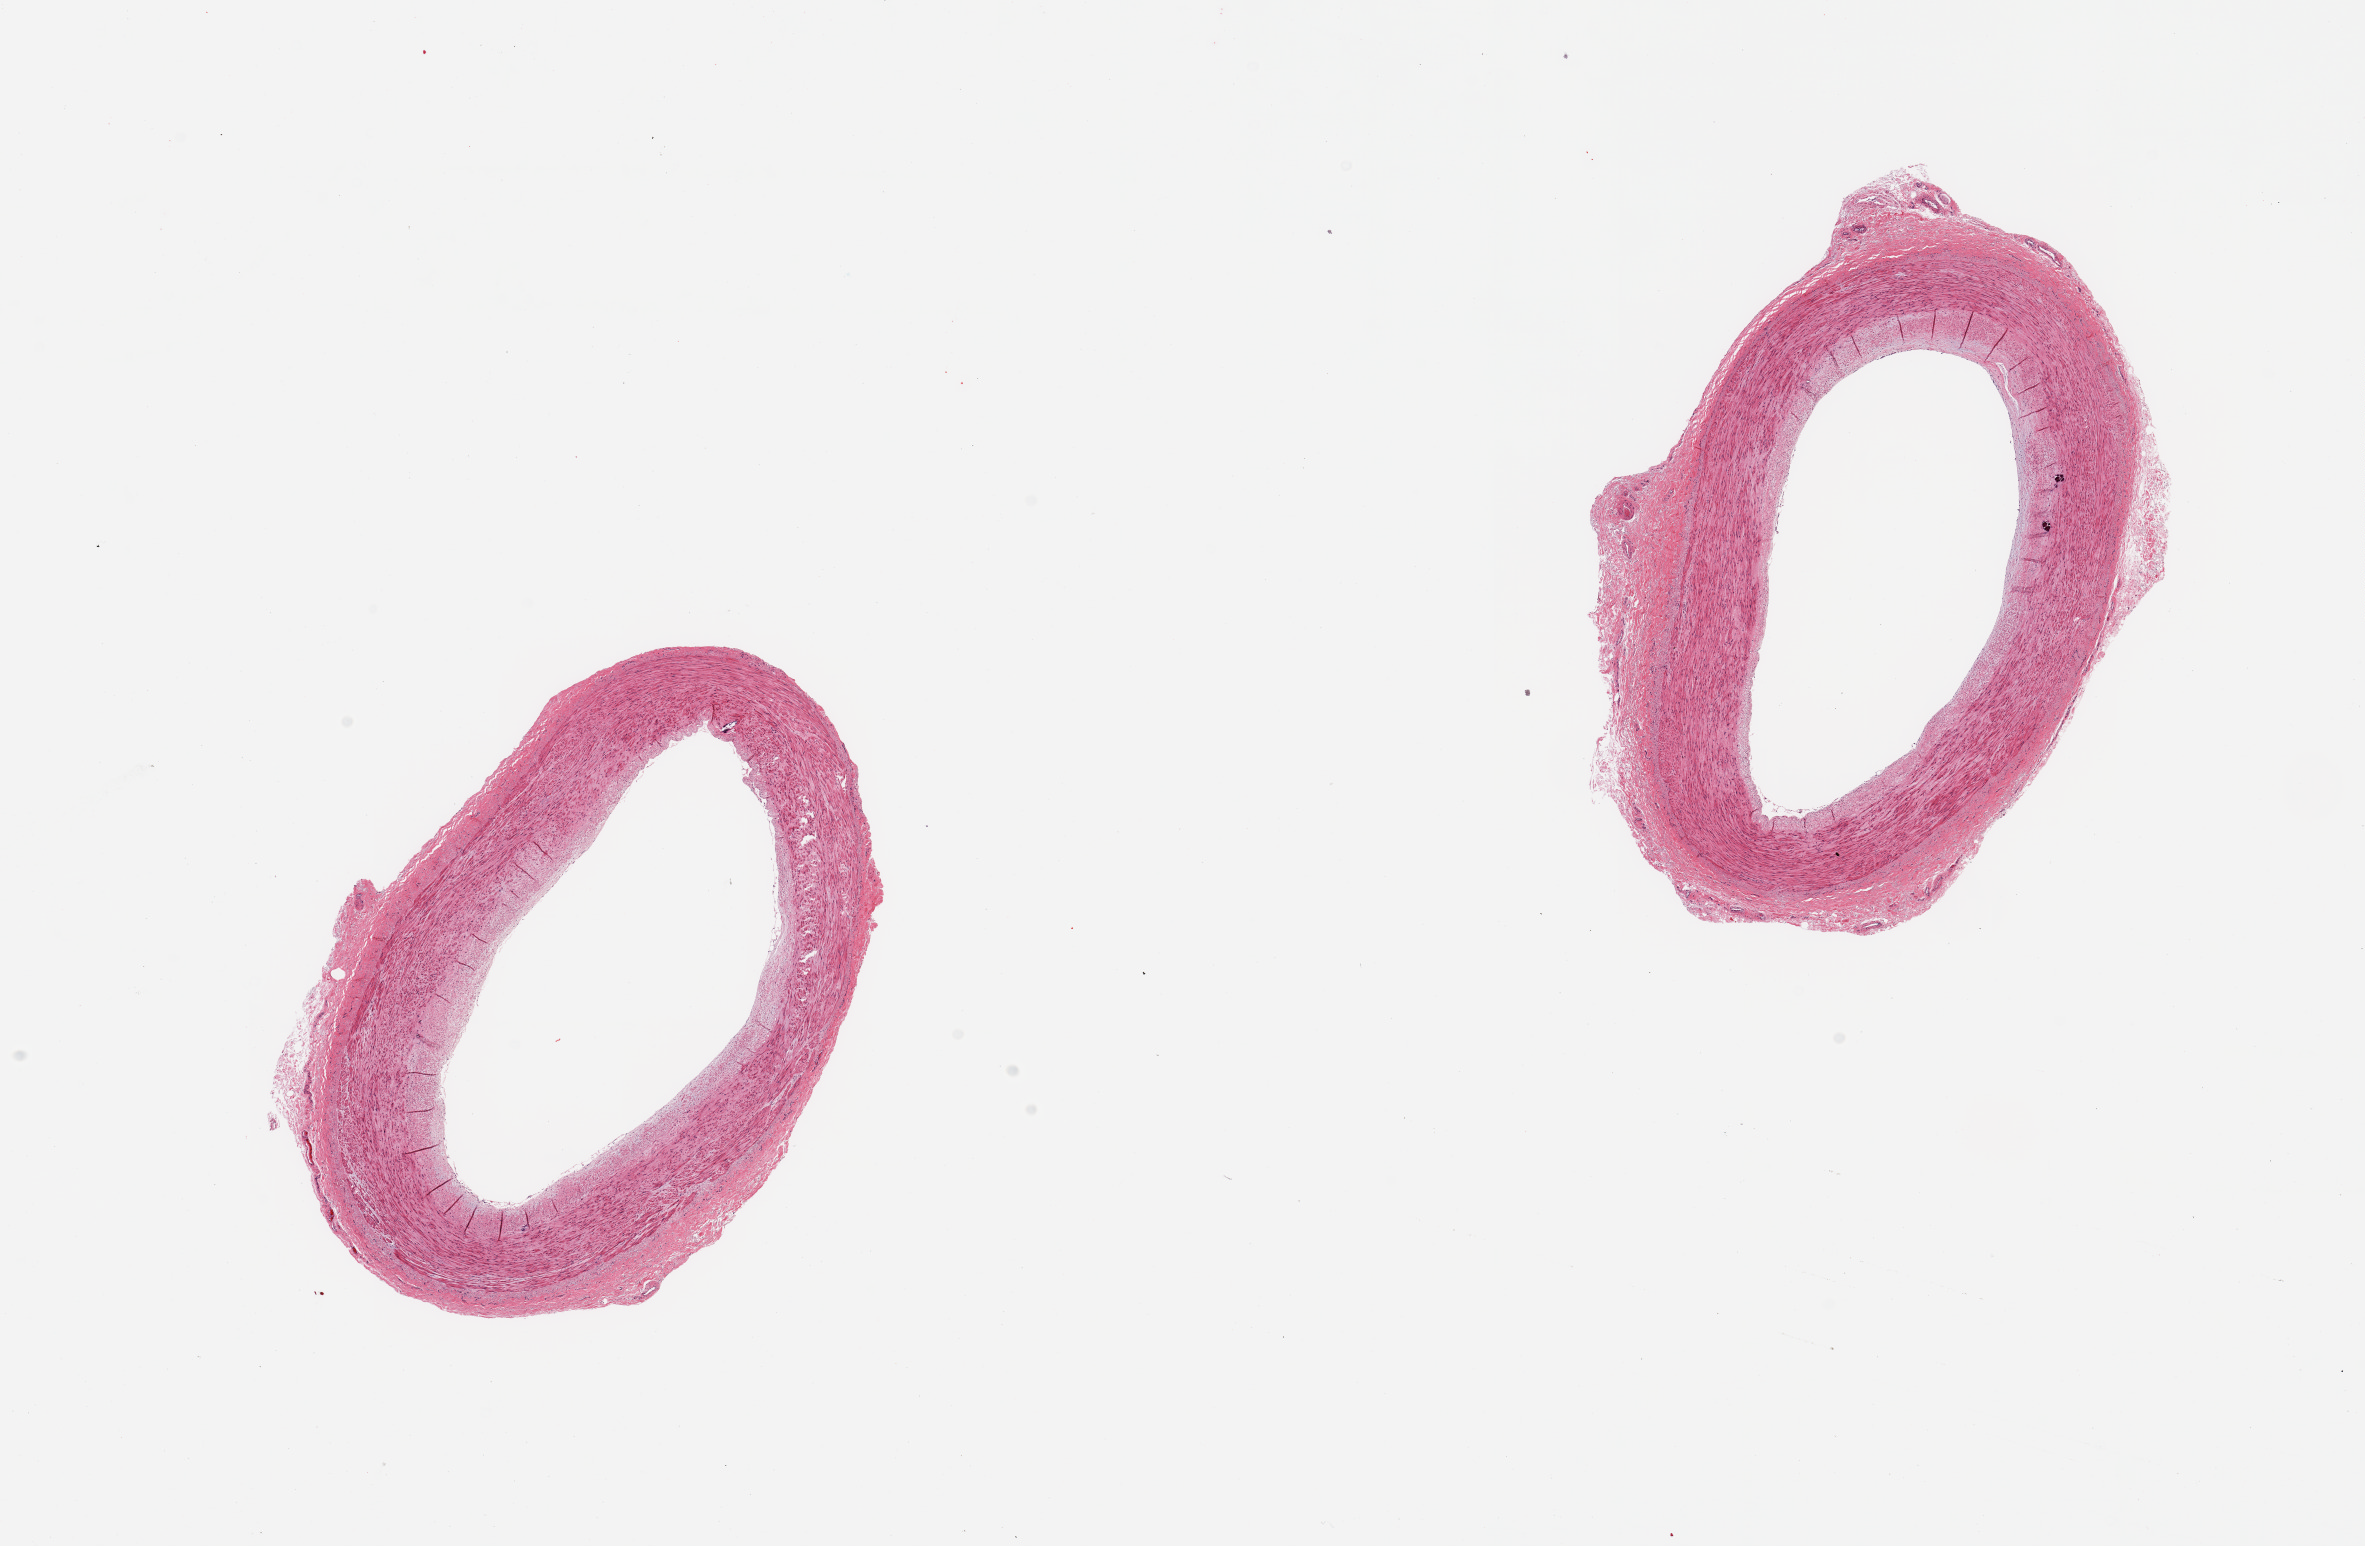
Digitized H&E-stained section, shown as a low-resolution overview of the whole scanned area (about 18.7 x 12.2 mm), PAXgene-fixed, paraffin-embedded tissue, section of tibial artery (target tissue), tissue donor sample. Donor sex: male.
Review note (as recorded): 2 pieces, no significant atherosis.